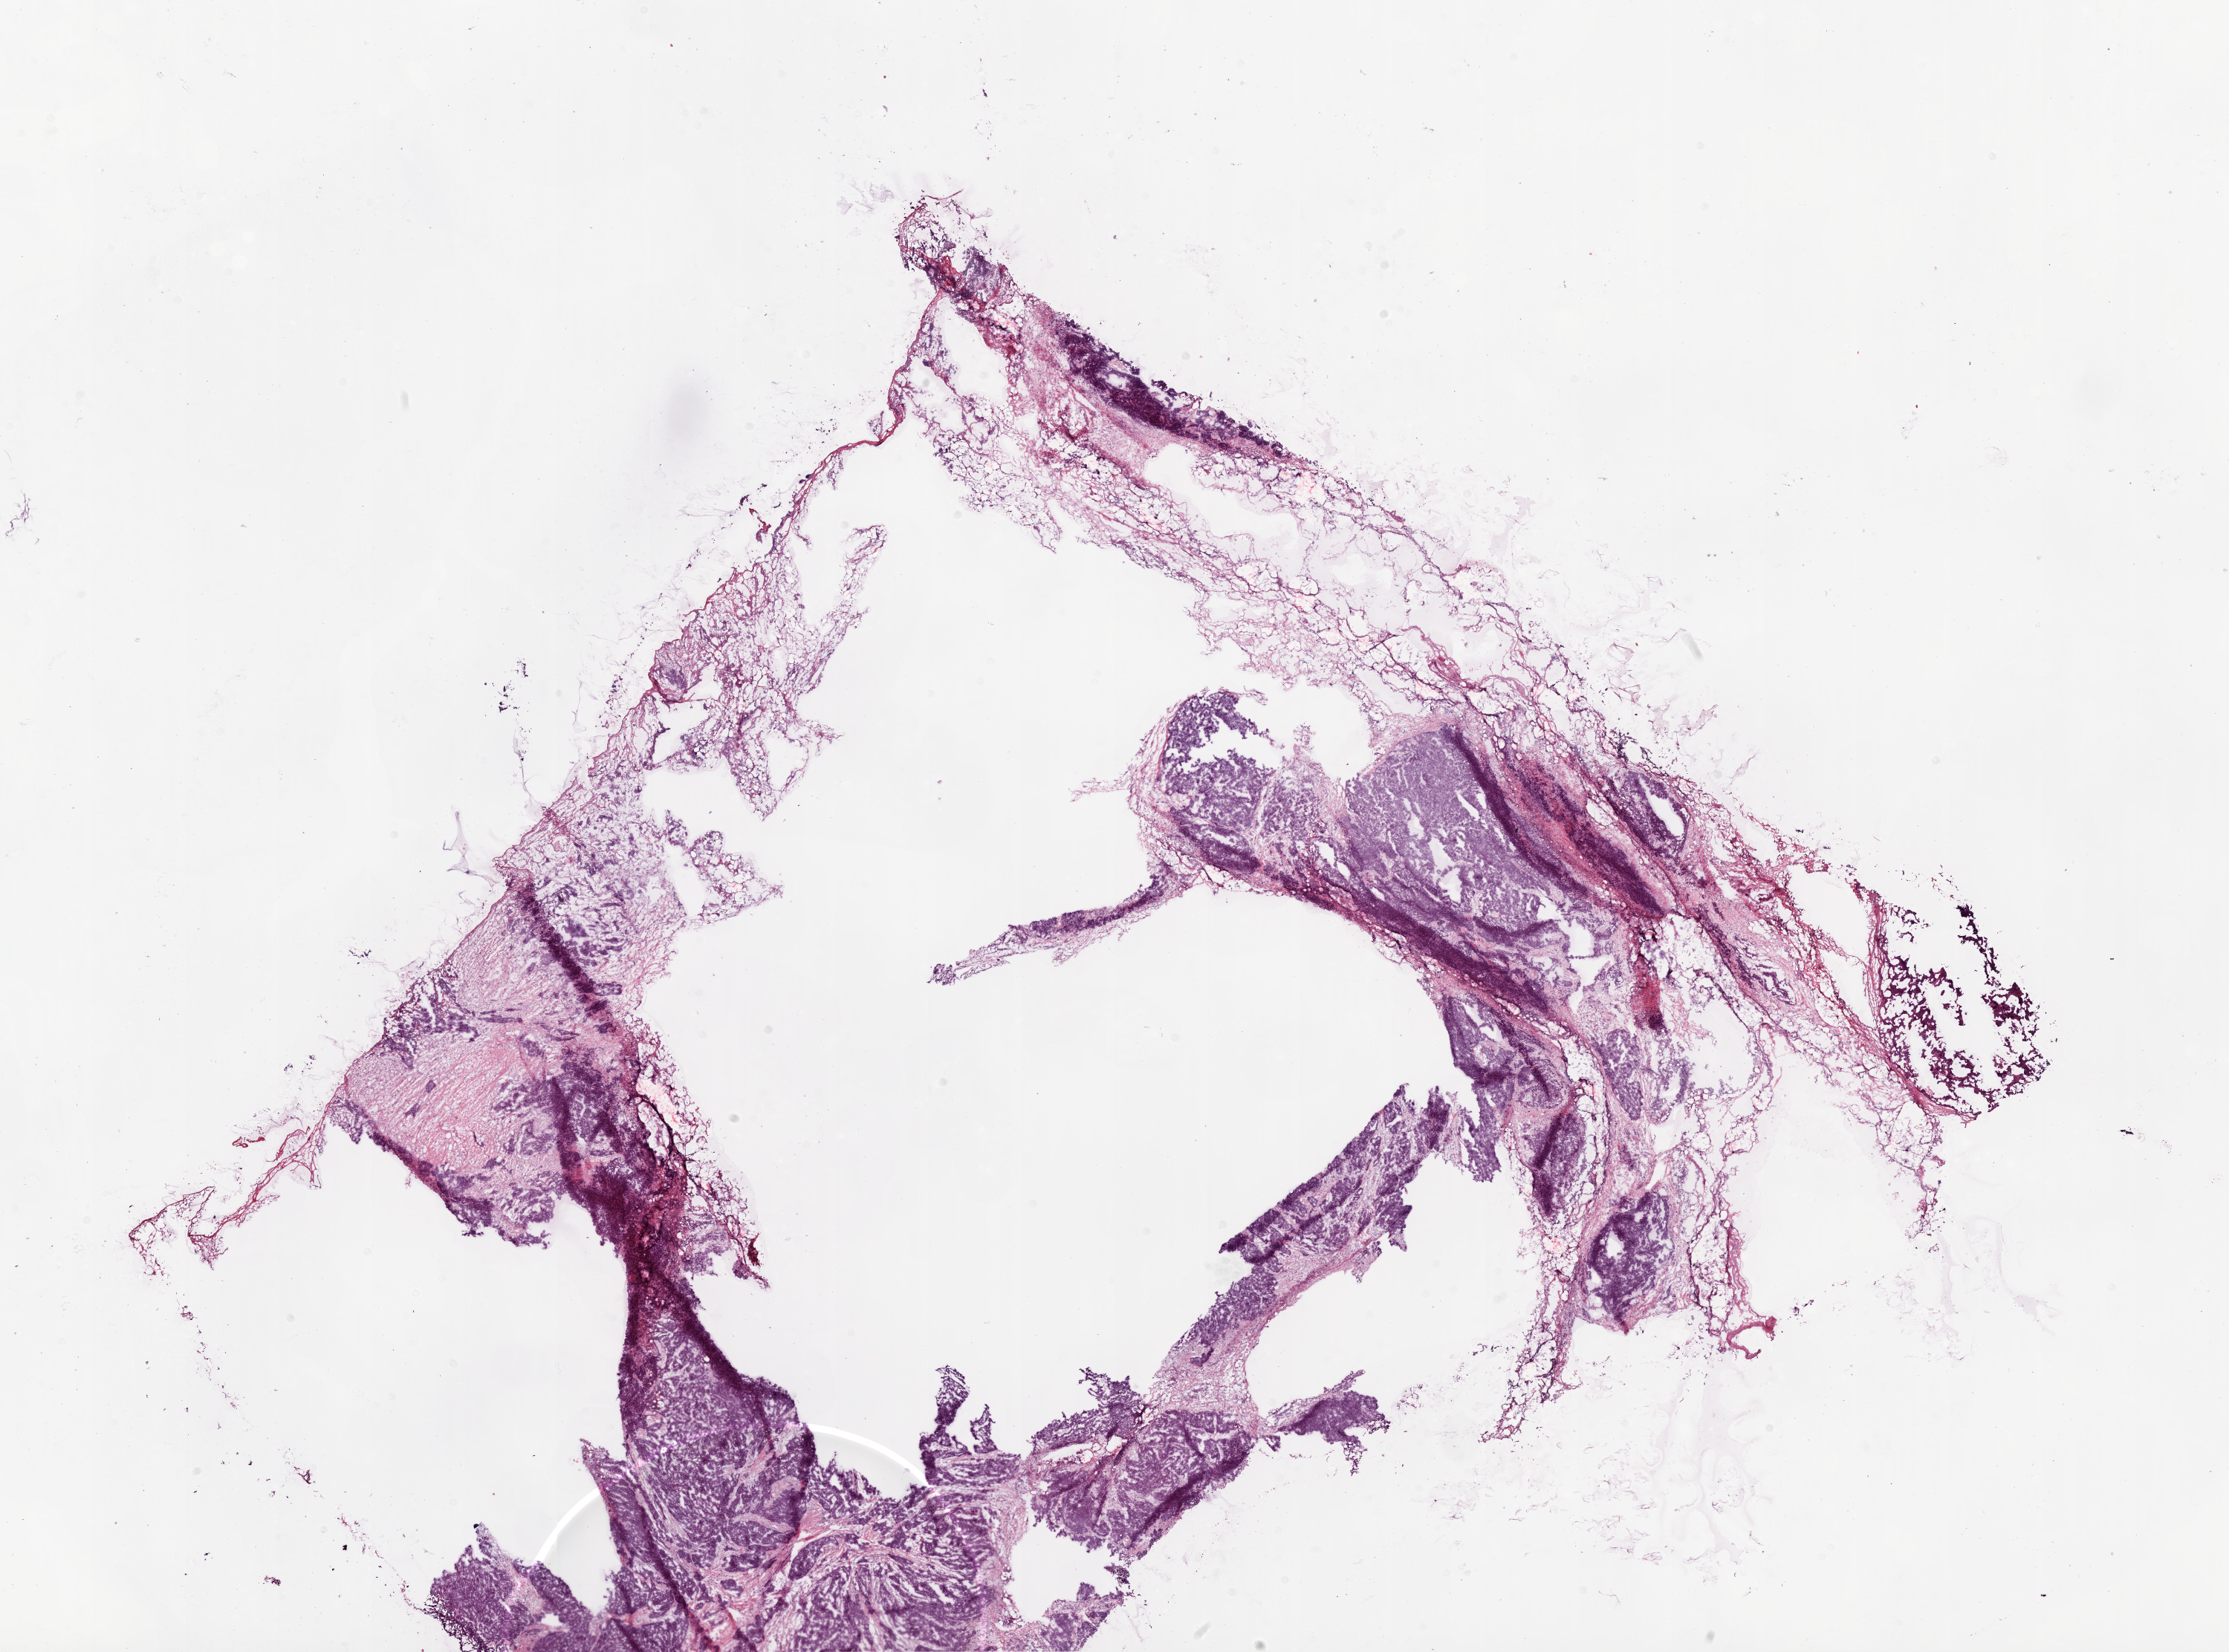
Digitized H&E tissue section (whole slide), whole scanned area (about 24.1 x 17.8 mm, slide scanned at 20x) shown as a low-resolution overview; frozen section from the bottom of the tissue portion; sample: primary tumour, ovary. Female, age 71 years at initial diagnosis. Histologic grade: G3 (poorly differentiated). Pathologist review of this section (percent, as recorded): tumour cells 70%, tumour nuclei 85%, normal cells 0%, stromal cells 30%, necrosis 0%. Inflammatory infiltration, as recorded: lymphocyte infiltration 5%, monocyte infiltration 0%, neutrophil infiltration 0%.
- histologic diagnosis: Serous cystadenocarcinoma, NOS
- FIGO stage: IIIC